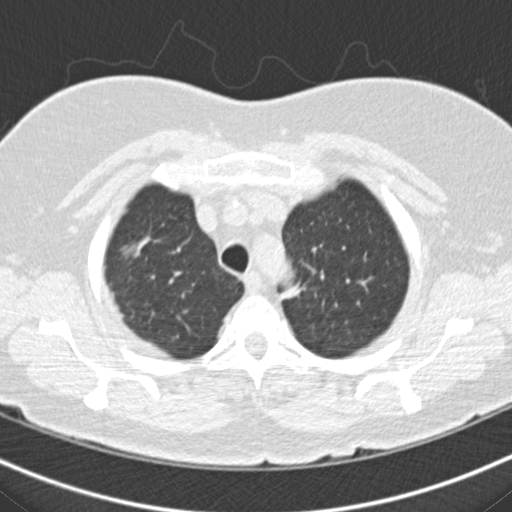
Low-dose screening chest CT, one axial slice; position 140 of 160 along the scan axis; reconstruction kernel B30f; 120 kVp; lung window (W 1500 / L -600 HU); 512 × 512 image matrix.
Annotated regions visible in this slice (manually delineated by an expert):
- lesion 3 (nodule, upper lobe of right lung): bounding box (x1, y1, x2, y2) in pixels: (130, 237, 146, 253)